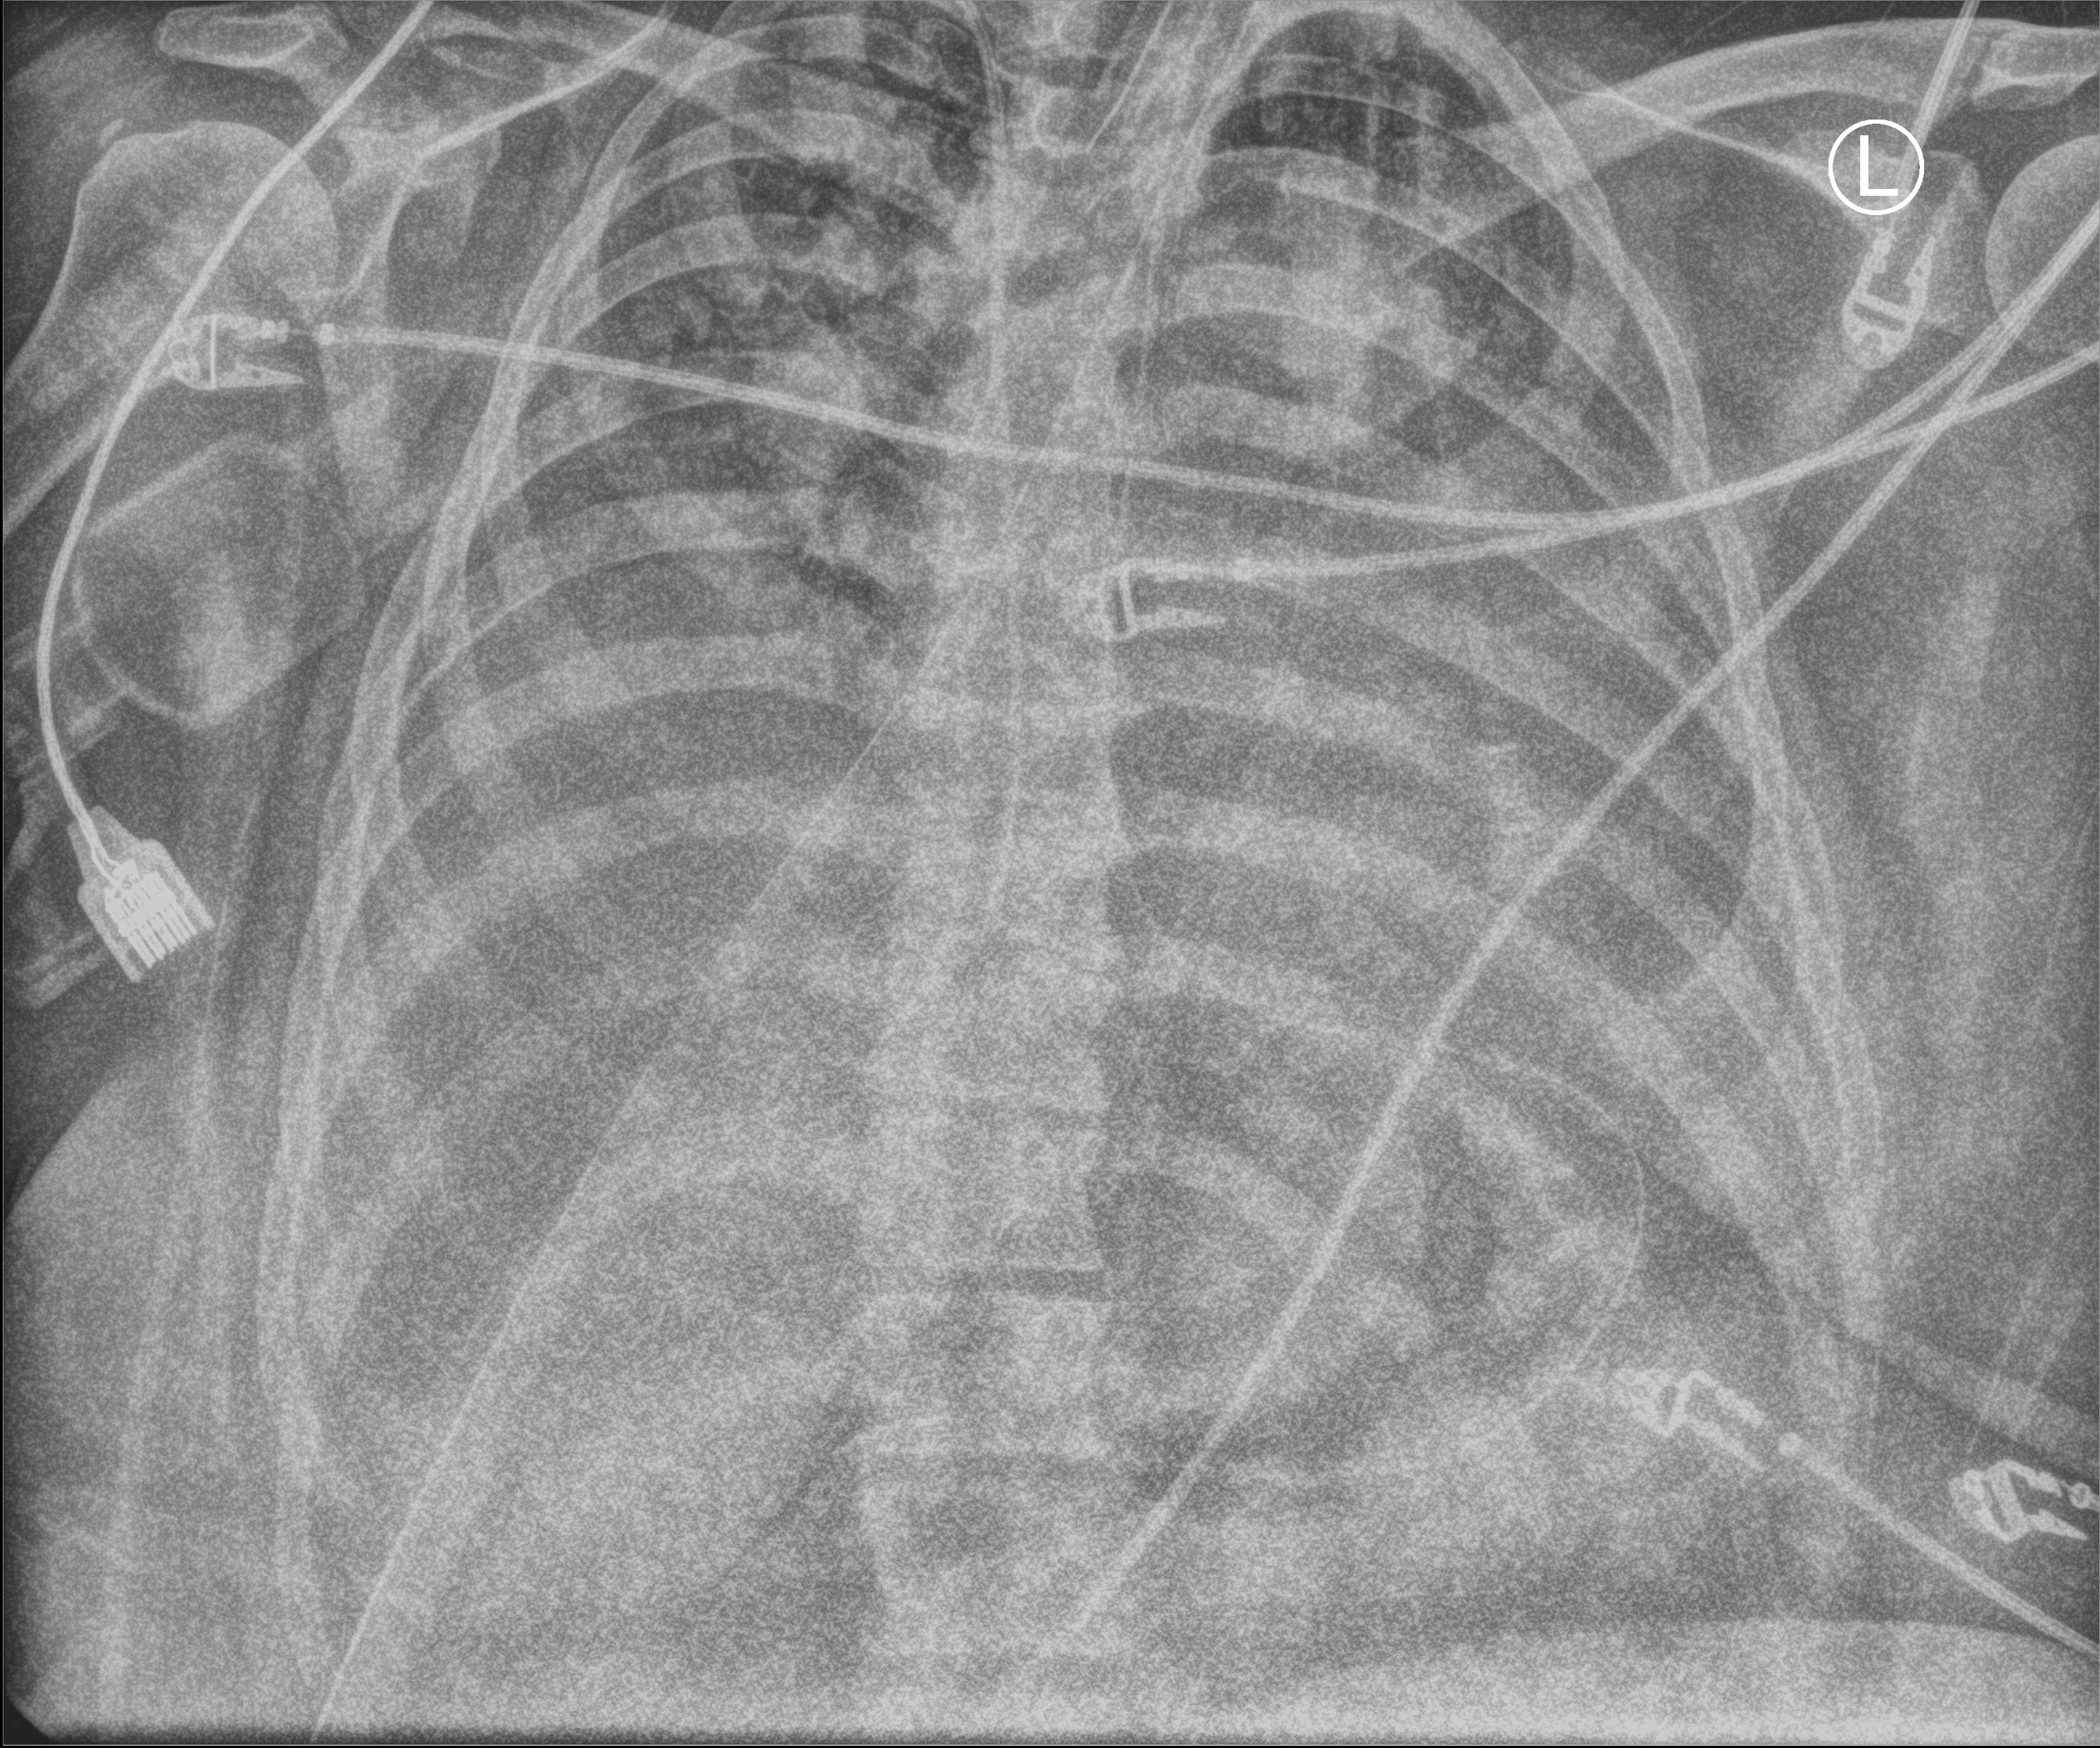
Portable chest radiograph. Patient hospitalised with COVID-19; female, aged 18–59 years.
Admission-level facts for this patient (not findings on this image; timing relative to this image not recorded): diabetes (admission record): no; other chronic lung disease (admission record): no; mechanically ventilated during this hospital stay: yes.